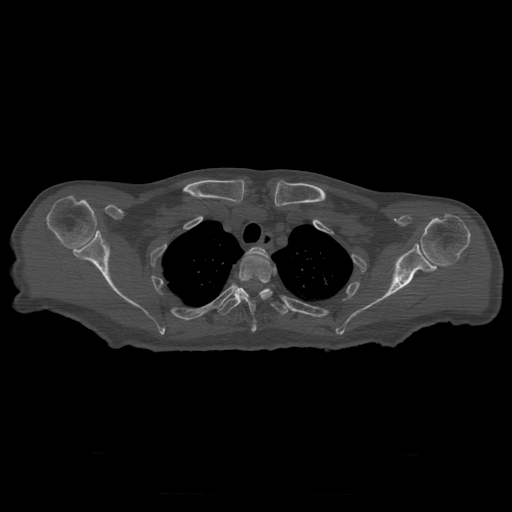
CT including the spine, one axial slice; position 254 of 397 along the scan axis; reconstruction kernel STANDARD; 120 kVp; bone window (W 1800 / L 400 HU); 1.25 mm slice thickness; 512 × 512 image matrix, field of view 510 × 510 mm. Patient age 73 years. Case-level facts recorded for this patient, not image findings: primary cancer: prostate.
Annotated regions visible in this slice (semi-automatically segmented with operator editing):
- T2 vertebra: bounding box (x1, y1, x2, y2) in pixels: (246, 247, 270, 260)
- T3 vertebra: (235, 253, 273, 332)
- T4 vertebra: (218, 288, 289, 315)